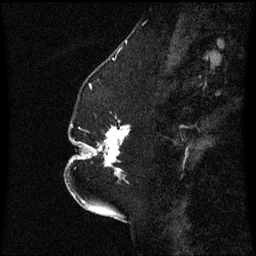
Breast MRI (dynamic contrast-enhanced), one sagittal slice; slice 21 of 60 in the series (ordered by position); dynamic contrast-enhanced series, image 2 of 3 at this slice position (ordered by acquisition); 1.5 T; TE 4.2 ms, TR 8.4 ms; 256 × 256 image matrix. Patient: female, 52 years. Case-level facts recorded for this patient, not image findings: setting: breast cancer imaged before/during neoadjuvant chemotherapy; receptor status: HR-positive, HER2-negative.
Annotated regions visible in this slice (semi-automatic segmentation, software-assisted and operator-edited):
- analysis volume of interest (the breast-tissue region the enhancement analysis was run in; not a lesion): bounding box <75,118,129,181> (left, top, right, bottom; pixels)
- tumour enhancement mask (voxels above the 70 % enhancement threshold inside the analysis volume of interest): <78,126,129,177>